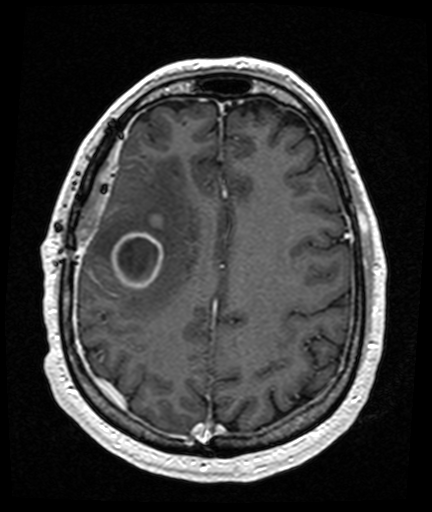
Brain MRI from a brain-tumour surgery series, one axial slice. Slice 53 of 176 in the series (ordered by position). T1-weighted post-contrast. 1 mm slice thickness. 432 × 512 image matrix, field of view 194 × 230 mm. Case-level facts recorded for this patient, not image findings: histopathology: Glioblastoma; WHO grade: 4; IDH mutation: no.
Outlined on this slice (expert manual segmentation):
- tumour: bounding box (x1, y1, x2, y2) in pixels: (113, 233, 163, 288)